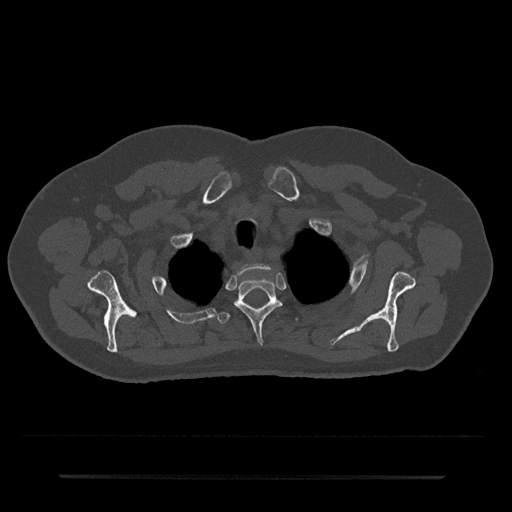
CT including the spine, one axial slice. Slice 602 of 797 in the series (ordered by position). Reconstruction kernel Br40s/3. Bone window (W 1800 / L 400 HU). 0.5 mm slice thickness. 512 × 512 image matrix. Male patient, age 69 years. Case-level facts recorded for this patient, not image findings: primary cancer: prostate.
Structures marked on this image (semi-automatic segmentation, software-assisted and operator-edited):
- T1 vertebra: bounding box (x1, y1, x2, y2) in pixels: (238, 264, 270, 275)
- T2 vertebra: (234, 278, 282, 345)
- T3 vertebra: (217, 300, 298, 324)